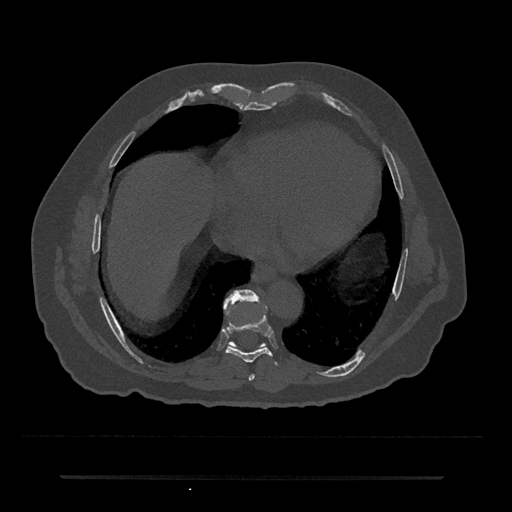
CT including the spine, one axial slice; position 319 of 797 along the scan axis; bone window (W 1800 / L 400 HU); 512 × 512 image matrix. Patient: male, 69 years. From the clinical record (not read from this slice): primary cancer: prostate.
Annotated regions visible in this slice (semi-automatically segmented with operator editing):
- T7 vertebra: bounding box <248,374,255,381> (left, top, right, bottom; pixels)
- T8 vertebra: <225,314,279,366>
- T9 vertebra: <226,290,259,344>